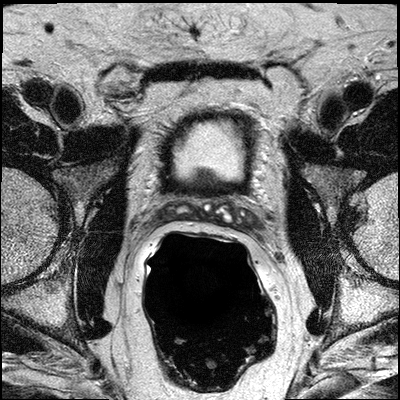
Multiparametric prostate MRI examination; 3 images, each a single mid-volume slice chosen by position (not for content). Treatment context recorded for this patient: No surgery, treatment with external beam radiation +/- androgen ablation treatment.
Image 1: axial T2-weighted image, slice 16 of 30.
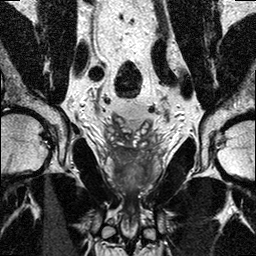
Image 2: T2-weighted coronal slice, slice 11 of 20, 3 mm slice thickness.
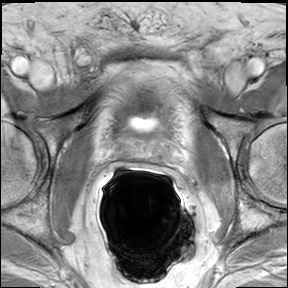
Image 3: DCE (dynamic gadolinium-enhanced) axial slice, slice 16 of 30, dynamic phase 5 of 8.
Radiologist's MRI report for this examination:
prostate has a maximal lateral diameter of 4.1 cm, a maximal craniocaudal diameter of 3.7 cm and a maximal AP diameter of 2.6 cm resulting in an estimated gland volume of 21 cc. The zonal anatomy is preserved. There signs of chronic prostatitis bilaterally. In the right lobe, midthird peripheral zone at 8 o'clock there is a small area of irregular geographic T2 hypointensity with highly suspicious enhancement (rapid wash-in, rapid wash out) on dynamic contrast enhanced sequences compatible with tumor (series 501 image 10). In the left midthird to the apex peripheral zone, at 5 o'clock, there is a geographic region of T2 hypointensity with suspicious contrast enhancement (series 704 image 59). Tumor extends to the capsule bilaterally and there may be capsular infiltration between 7 o'clock and 5 o'clock. There is no manifest extracapsular tumor mass. No evidence for involvement of the neurovascular bundle on either side. Seminal vesicles are partially collapsed, which limits detection for tumor infiltration. There are slightly thickened walls. No discrete intraluminal tumor masses. No evidence of involvement of bladder neck and rectal wall. No suspiciously enlarged obturator and iliac lymph nodes. IMPRESSION: 1. Bilateral prostate cancer. Right midthird peripheral zone 7 o'clock infiltrative tumor abutting the capsule. Left midthird to the apex peripheral zone, at 5 o'clock infiltrative tumor abutting the capsule. There is possible capsular infiltration between 7 o'clock and 5 o'clock. 2. No manifest extracapsular tumor mass or neurovascular bundle involvement. 3. Minimally filled seminal vesicles limiting evaluation for tumor infiltration, although there are no intraluminal tumor masses

Prostate biopsy pathology (as recorded):
specimen is submitted entirely in six cassettes.1-right pz, 2-right pz/tz, 3-right apex, 4-left pz, 5-left pz/tz, 6-left apex. 1. RIGHT PZ: PROSTATIC ADENOCARCINOMA, GLEASON SCORE 3+3=6/10, INVOLVING THREE OF MULTIPLE CORES, AND 15% OF TOTAL TISSUE. 2. RIGHT PZ/TZ: PROSTATIC ADENOCARCINOMA, GLEASON SCORE 3+3=6/10, INVOLVING ONE OF TWO CORES, AND 5% OF TOTAL TISSUE. 3. RIGHT APEX: PROSTATIC ADENOCARCINOMA, GLEASON SCORE 3+4=7/10, INVOLVING ONE OF ONE CORE, AND 25% OF TOTAL TISSUE. 4. LEFT PZ: PROSTATIC ADENOCARCINOMA, GLEASON SCORE 3+4=7/10, INVOLVING THREE OF THREE CORES, AND 60% OF TOTAL TISSUE. PERINEURAL INVASION IS SEEN. 5. LEFT PZ/TZ: PROSTATIC ADENOCARCINOMA, GLEASON SCORE 4+3=7/10, INVOLVING TWO OF TWO CORES, AND 70% OF TOTAL TISSUE. 6. LEFT APEX: PROSTATIC ADENOCARCINOMA, GLEASON SCORE 3+4=7/10, INVOLVING ONE OF ONE CORE, AND 60% OF TOTAL TISSUE.